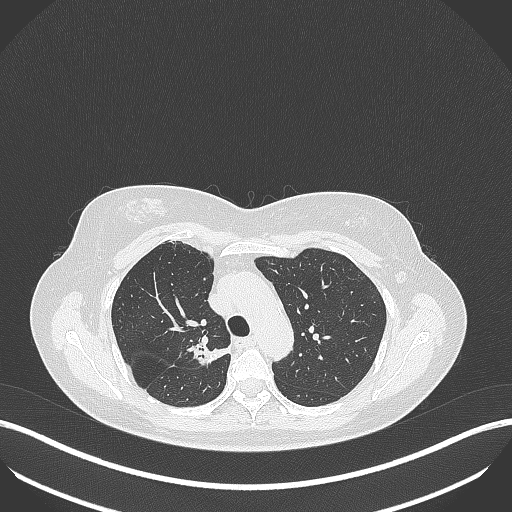
Chest CT, one axial slice. Position 284 of 386 along the scan axis. 120 kVp. Lung window (W 1500 / L -600 HU). 1 mm slice thickness. 512 × 512 image matrix. Patient: female, 65 years. Case-level facts recorded for this patient, not image findings: clinical TNM (as recorded): T1b N0 M0; histopathological grade: G2.
Annotated regions visible in this slice (rectangle marked by the reading radiologist):
- lung tumour (recorded histology: adenocarcinoma): bounding box (x1, y1, x2, y2) in pixels: (181, 336, 232, 369)